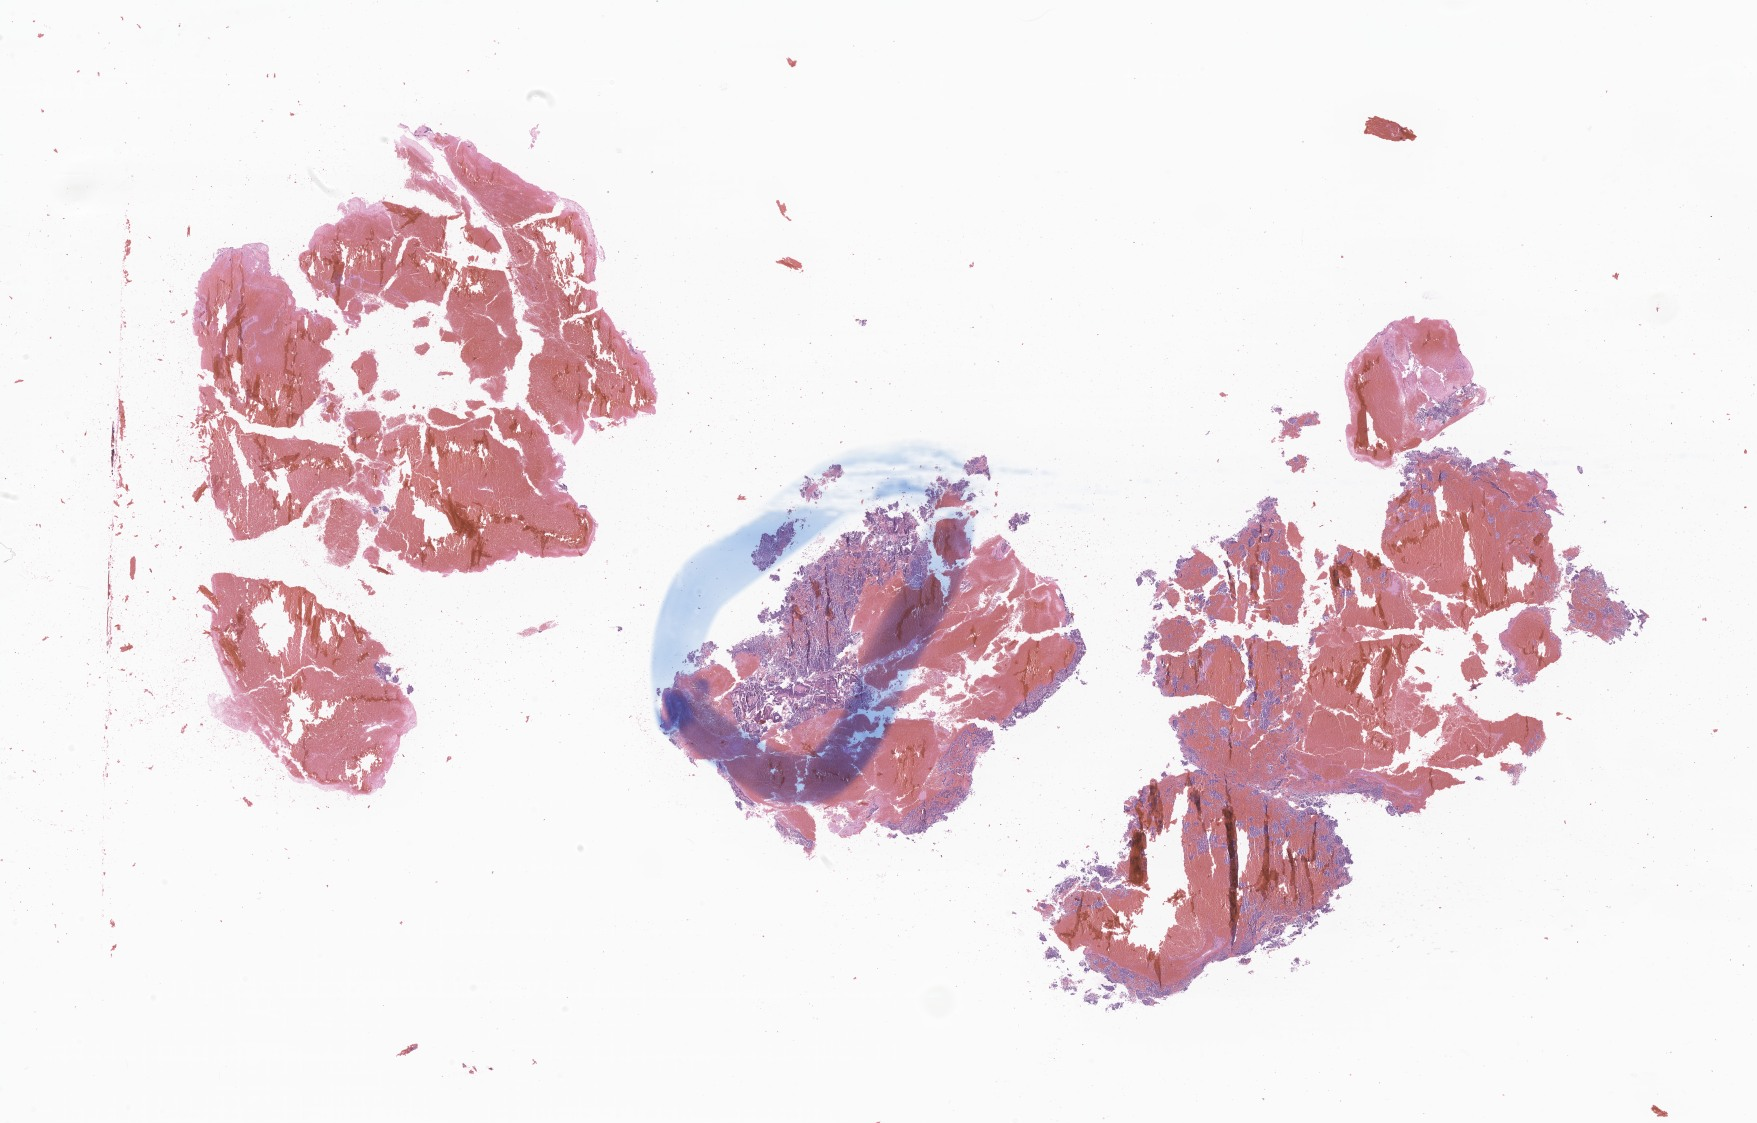
H&E whole-slide image of tumor tissue from the brain, a low-resolution overview of the entire scanned area, about 29.6 x 18.9 mm. Formalin-fixed, paraffin-embedded (FFPE) tissue. Patient female; age 55 months (4 years 7 months).
Diagnosis (ICD-O-3 morphology term): Medulloblastoma, NOS.